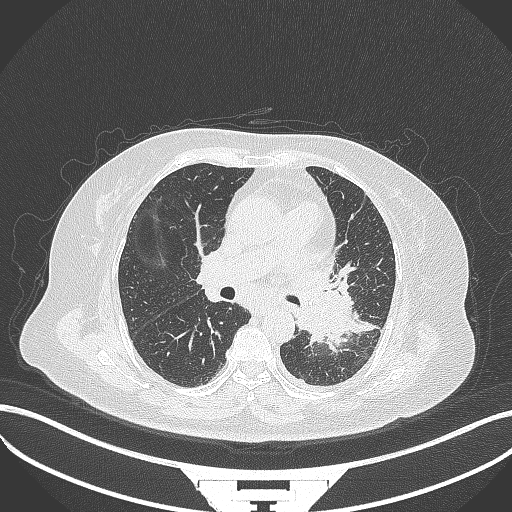
Chest CT, one axial slice. Slice 194 of 322 in the series (ordered by position). 120 kVp. Lung window (W 1500 / L -600 HU). 512 × 512 image matrix, field of view 400 × 400 mm. Patient: female, 69 years. From the clinical record (not read from this slice): clinical TNM (as recorded): T2b N3 M1.
Annotated regions visible in this slice (rectangle marked by the reading radiologist):
- lung tumour (recorded histology: adenocarcinoma): bounding box <294,282,352,347> (left, top, right, bottom; pixels)